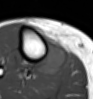
MRI of an extremity soft-tissue mass, one axial slice. MR volume resampled by the dataset authors to the PET/CT grid (not the native acquisition matrix). 93 × 99 image matrix, field of view 91 × 97 mm. Female patient. From the clinical record (not read from this slice): histological type: undifferentiated – high grade; grade: high; site of the primary tumour: right thigh.
Annotated regions visible in this slice (expert contour drawn on MRI and transferred to this co-registered scan by the dataset authors):
- gross tumour volume (mass): bounding box <36,39,67,76> (left, top, right, bottom; pixels)